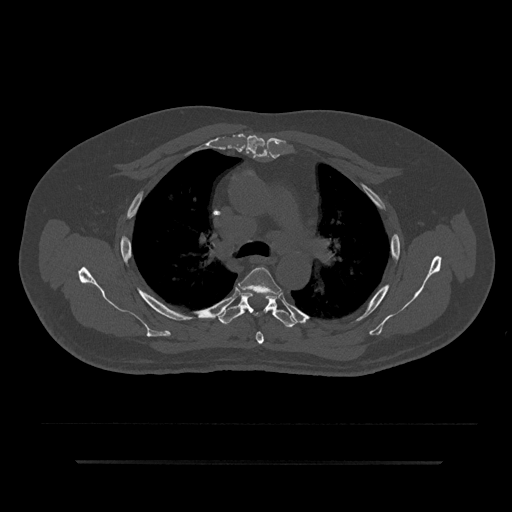
CT including the spine, one axial slice. Slice 594 of 797 in the series (ordered by position). 120 kVp. Bone window (W 1800 / L 400 HU). 0.5 mm slice thickness. 512 × 512 image matrix, field of view 464 × 464 mm. Male patient, age 59 years. From the clinical record (not read from this slice): primary cancer: bile ducts; vertebrae with lytic lesions (as recorded): T10.
Annotated regions visible in this slice (semi-automatic segmentation, software-assisted and operator-edited):
- T4 vertebra: bounding box [x1, y1, x2, y2] px = [238, 267, 281, 344]
- T5 vertebra: [219, 292, 298, 327]